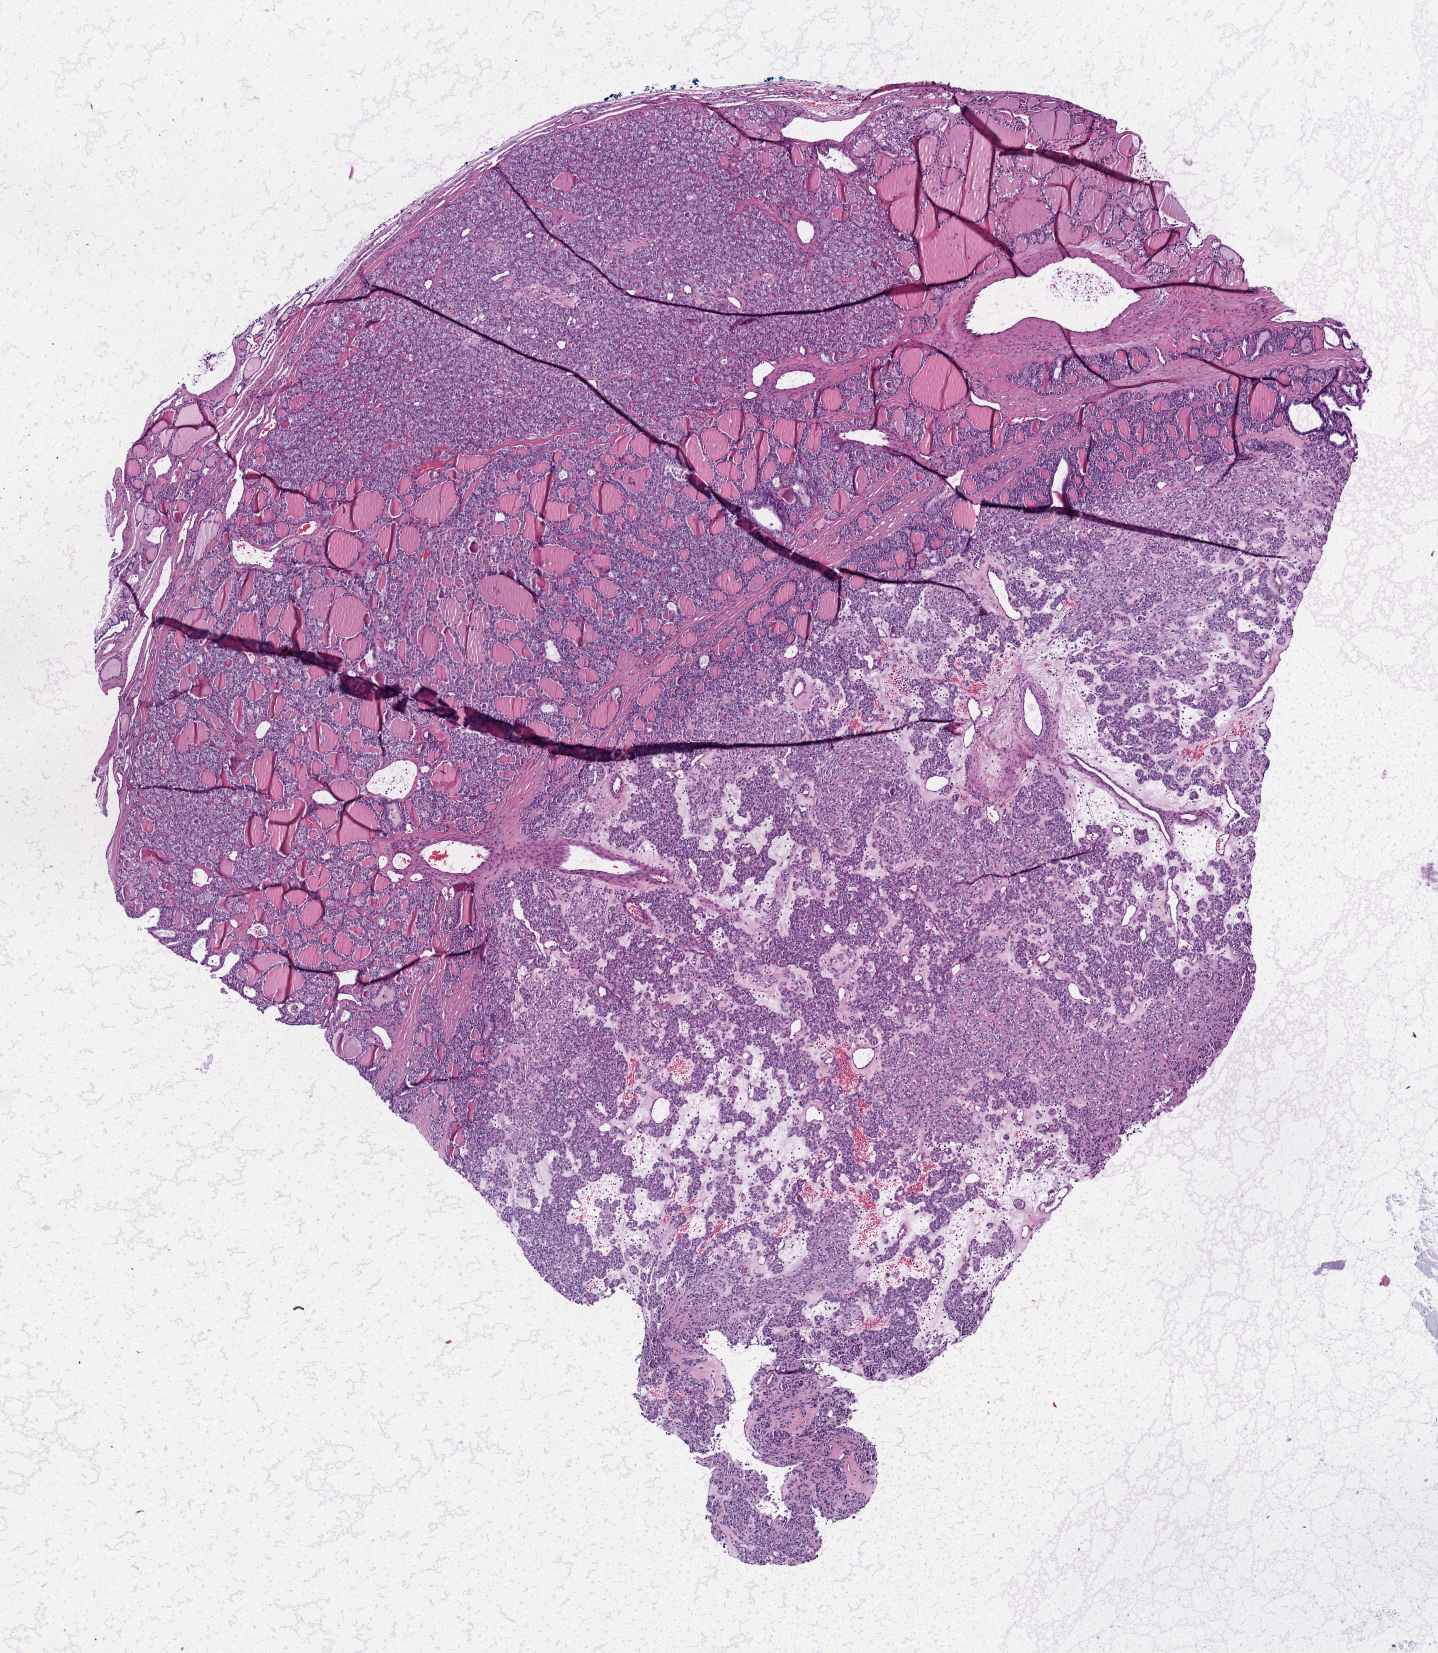
Digitized H&E tissue section (whole slide), shown as a low-resolution overview of the whole scanned area (about 5.8 x 6.7 mm, from a 40x scan), formalin-fixed paraffin-embedded (FFPE) diagnostic section, thyroid, primary tumour sample. Patient: male, age at initial diagnosis 54 years.
• TNM: T2 NX MX
• laterality: midline
• diagnosis: Papillary adenocarcinoma, NOS (thyroid gland)
• AJCC pathologic stage: II (7th edition)